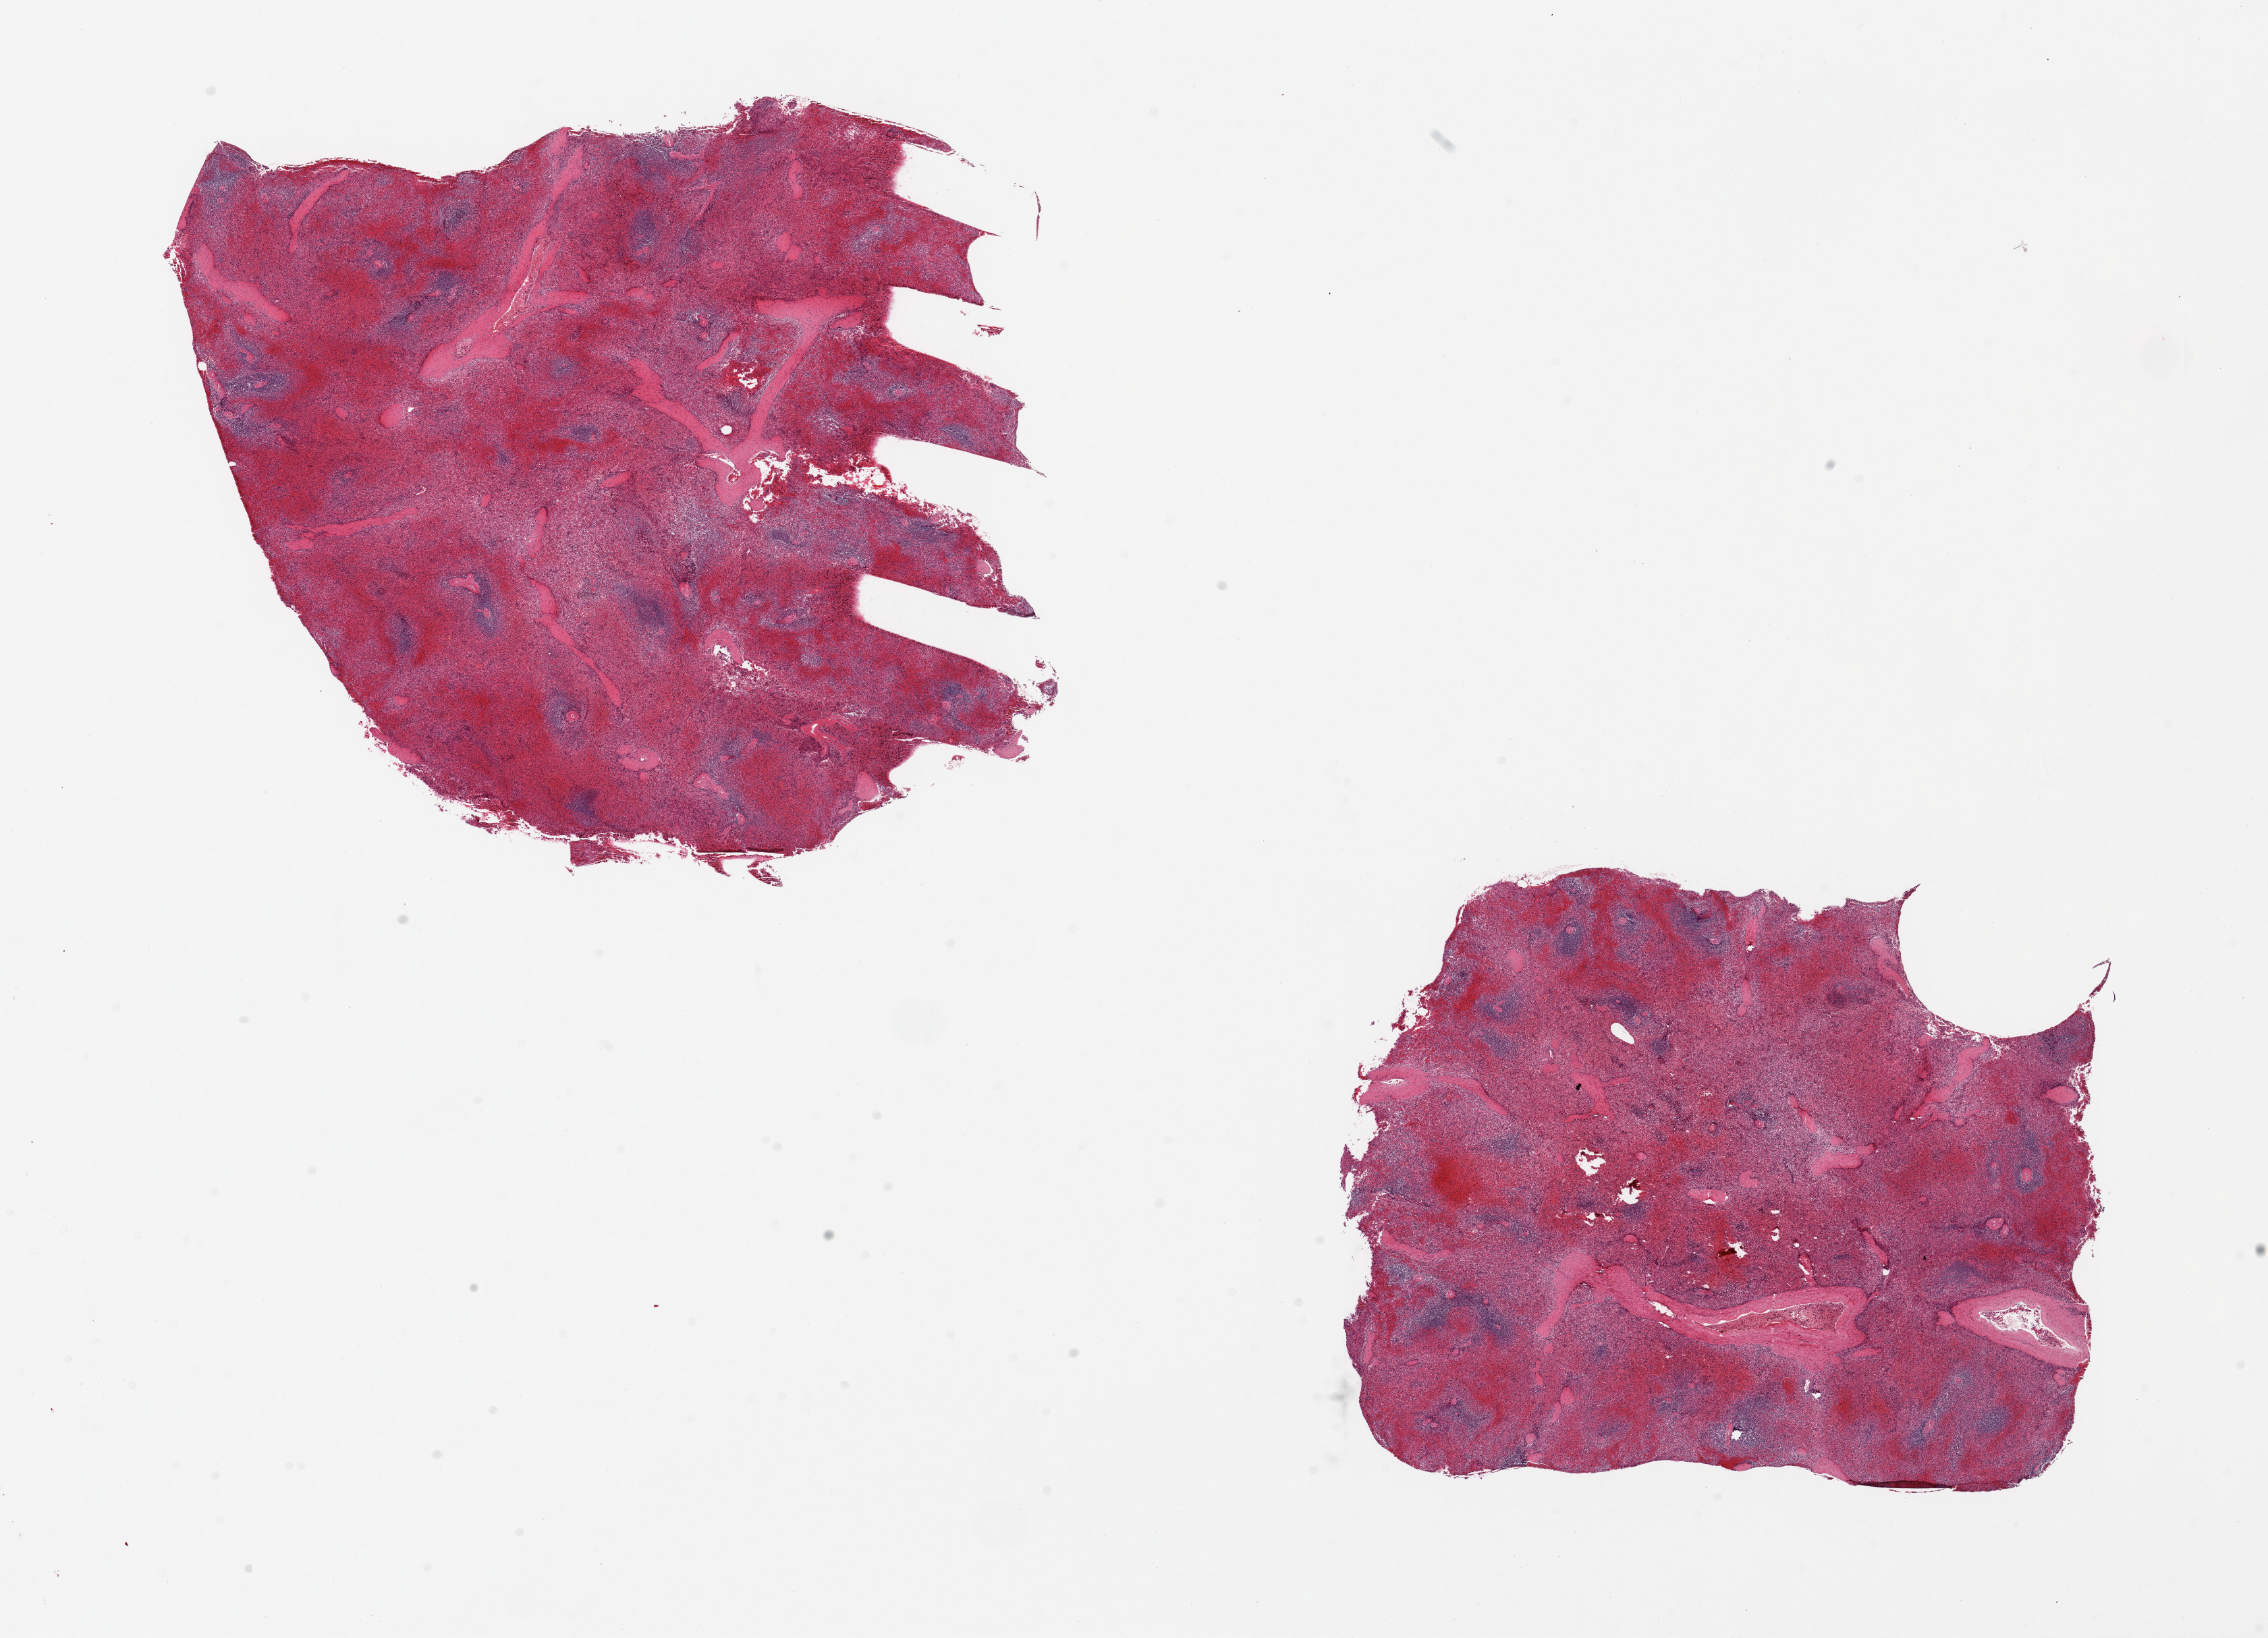
Hematoxylin and eosin (H&E) whole-slide image, brightfield, a low-resolution overview of the entire scanned area, about 26.6 x 19.2 mm (slide scanned at 20x), PAXgene-fixed, paraffin-embedded tissue, target tissue: spleen, donor tissue sample. Donor: male.
- reviewer comment on this tissue sample: 2 pieces. Passive congestion